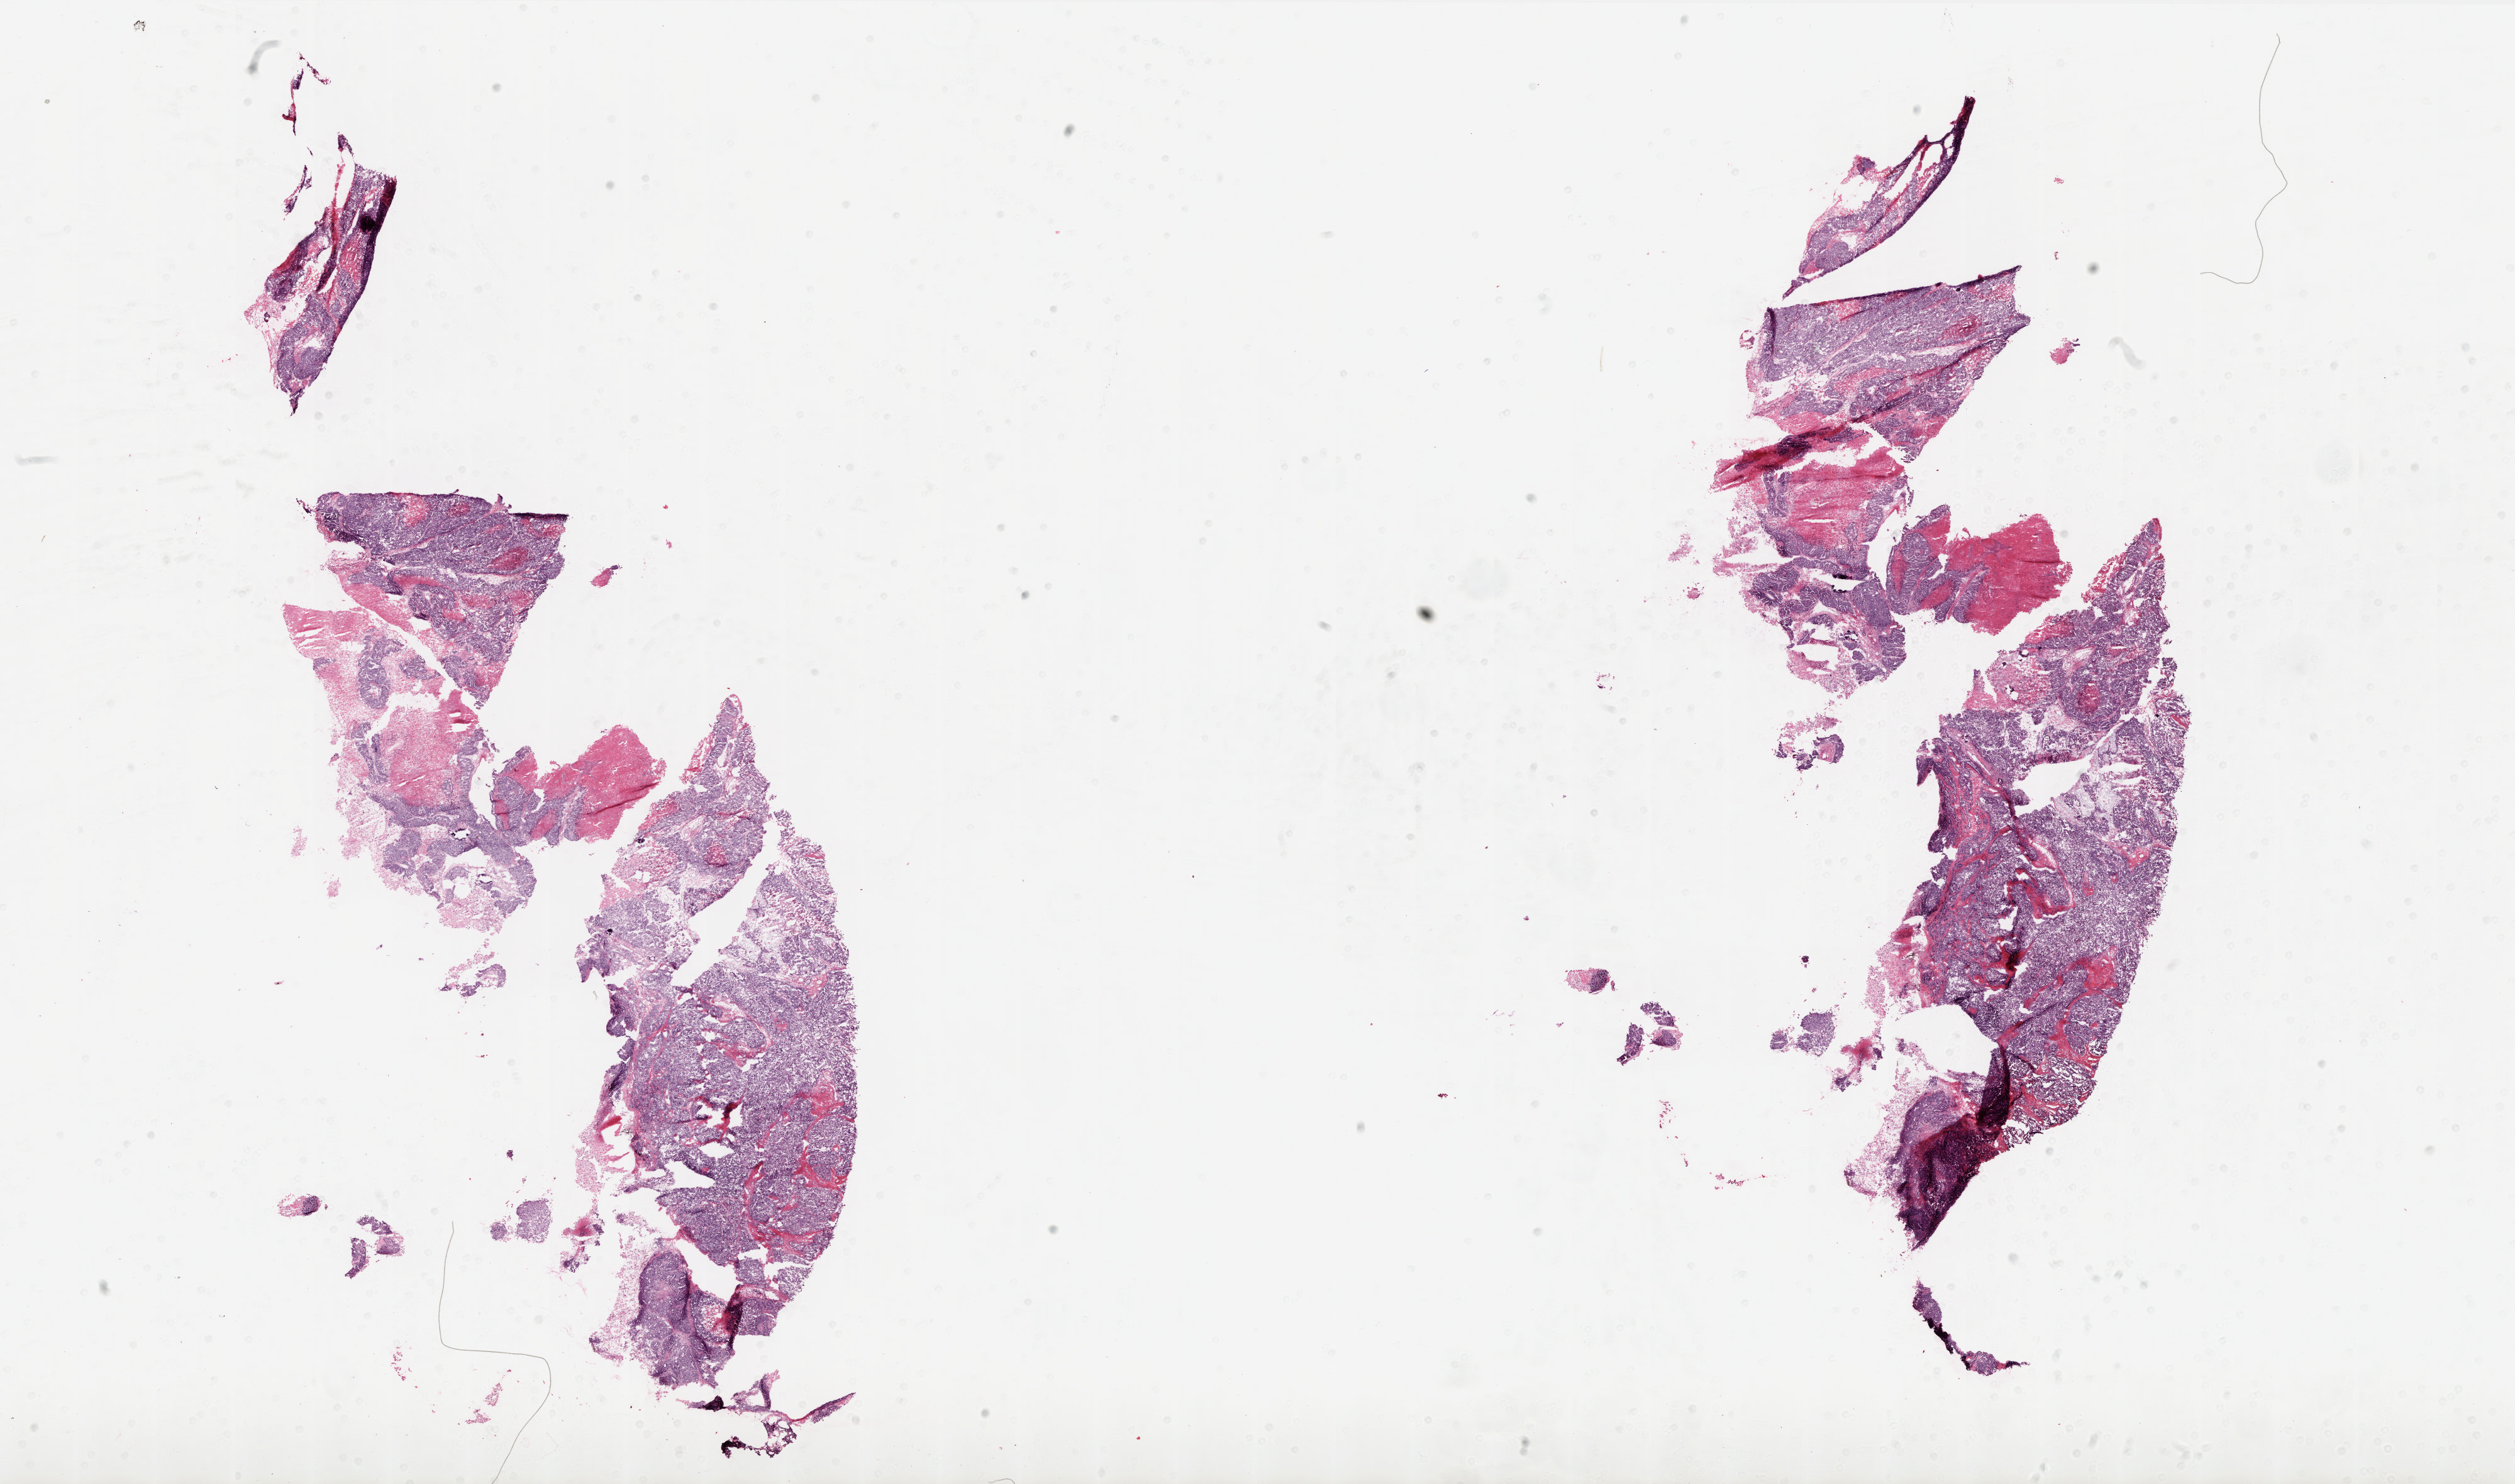
Digitized H&E-stained tissue section (whole slide), a low-resolution overview of the entire scanned area, about 31.9 x 18.8 mm; frozen section from the top of the tissue portion; primary tumour sample from the ovary. Patient: female, age at initial diagnosis 79 years.
Histologic diagnosis: Serous cystadenocarcinoma, NOS.